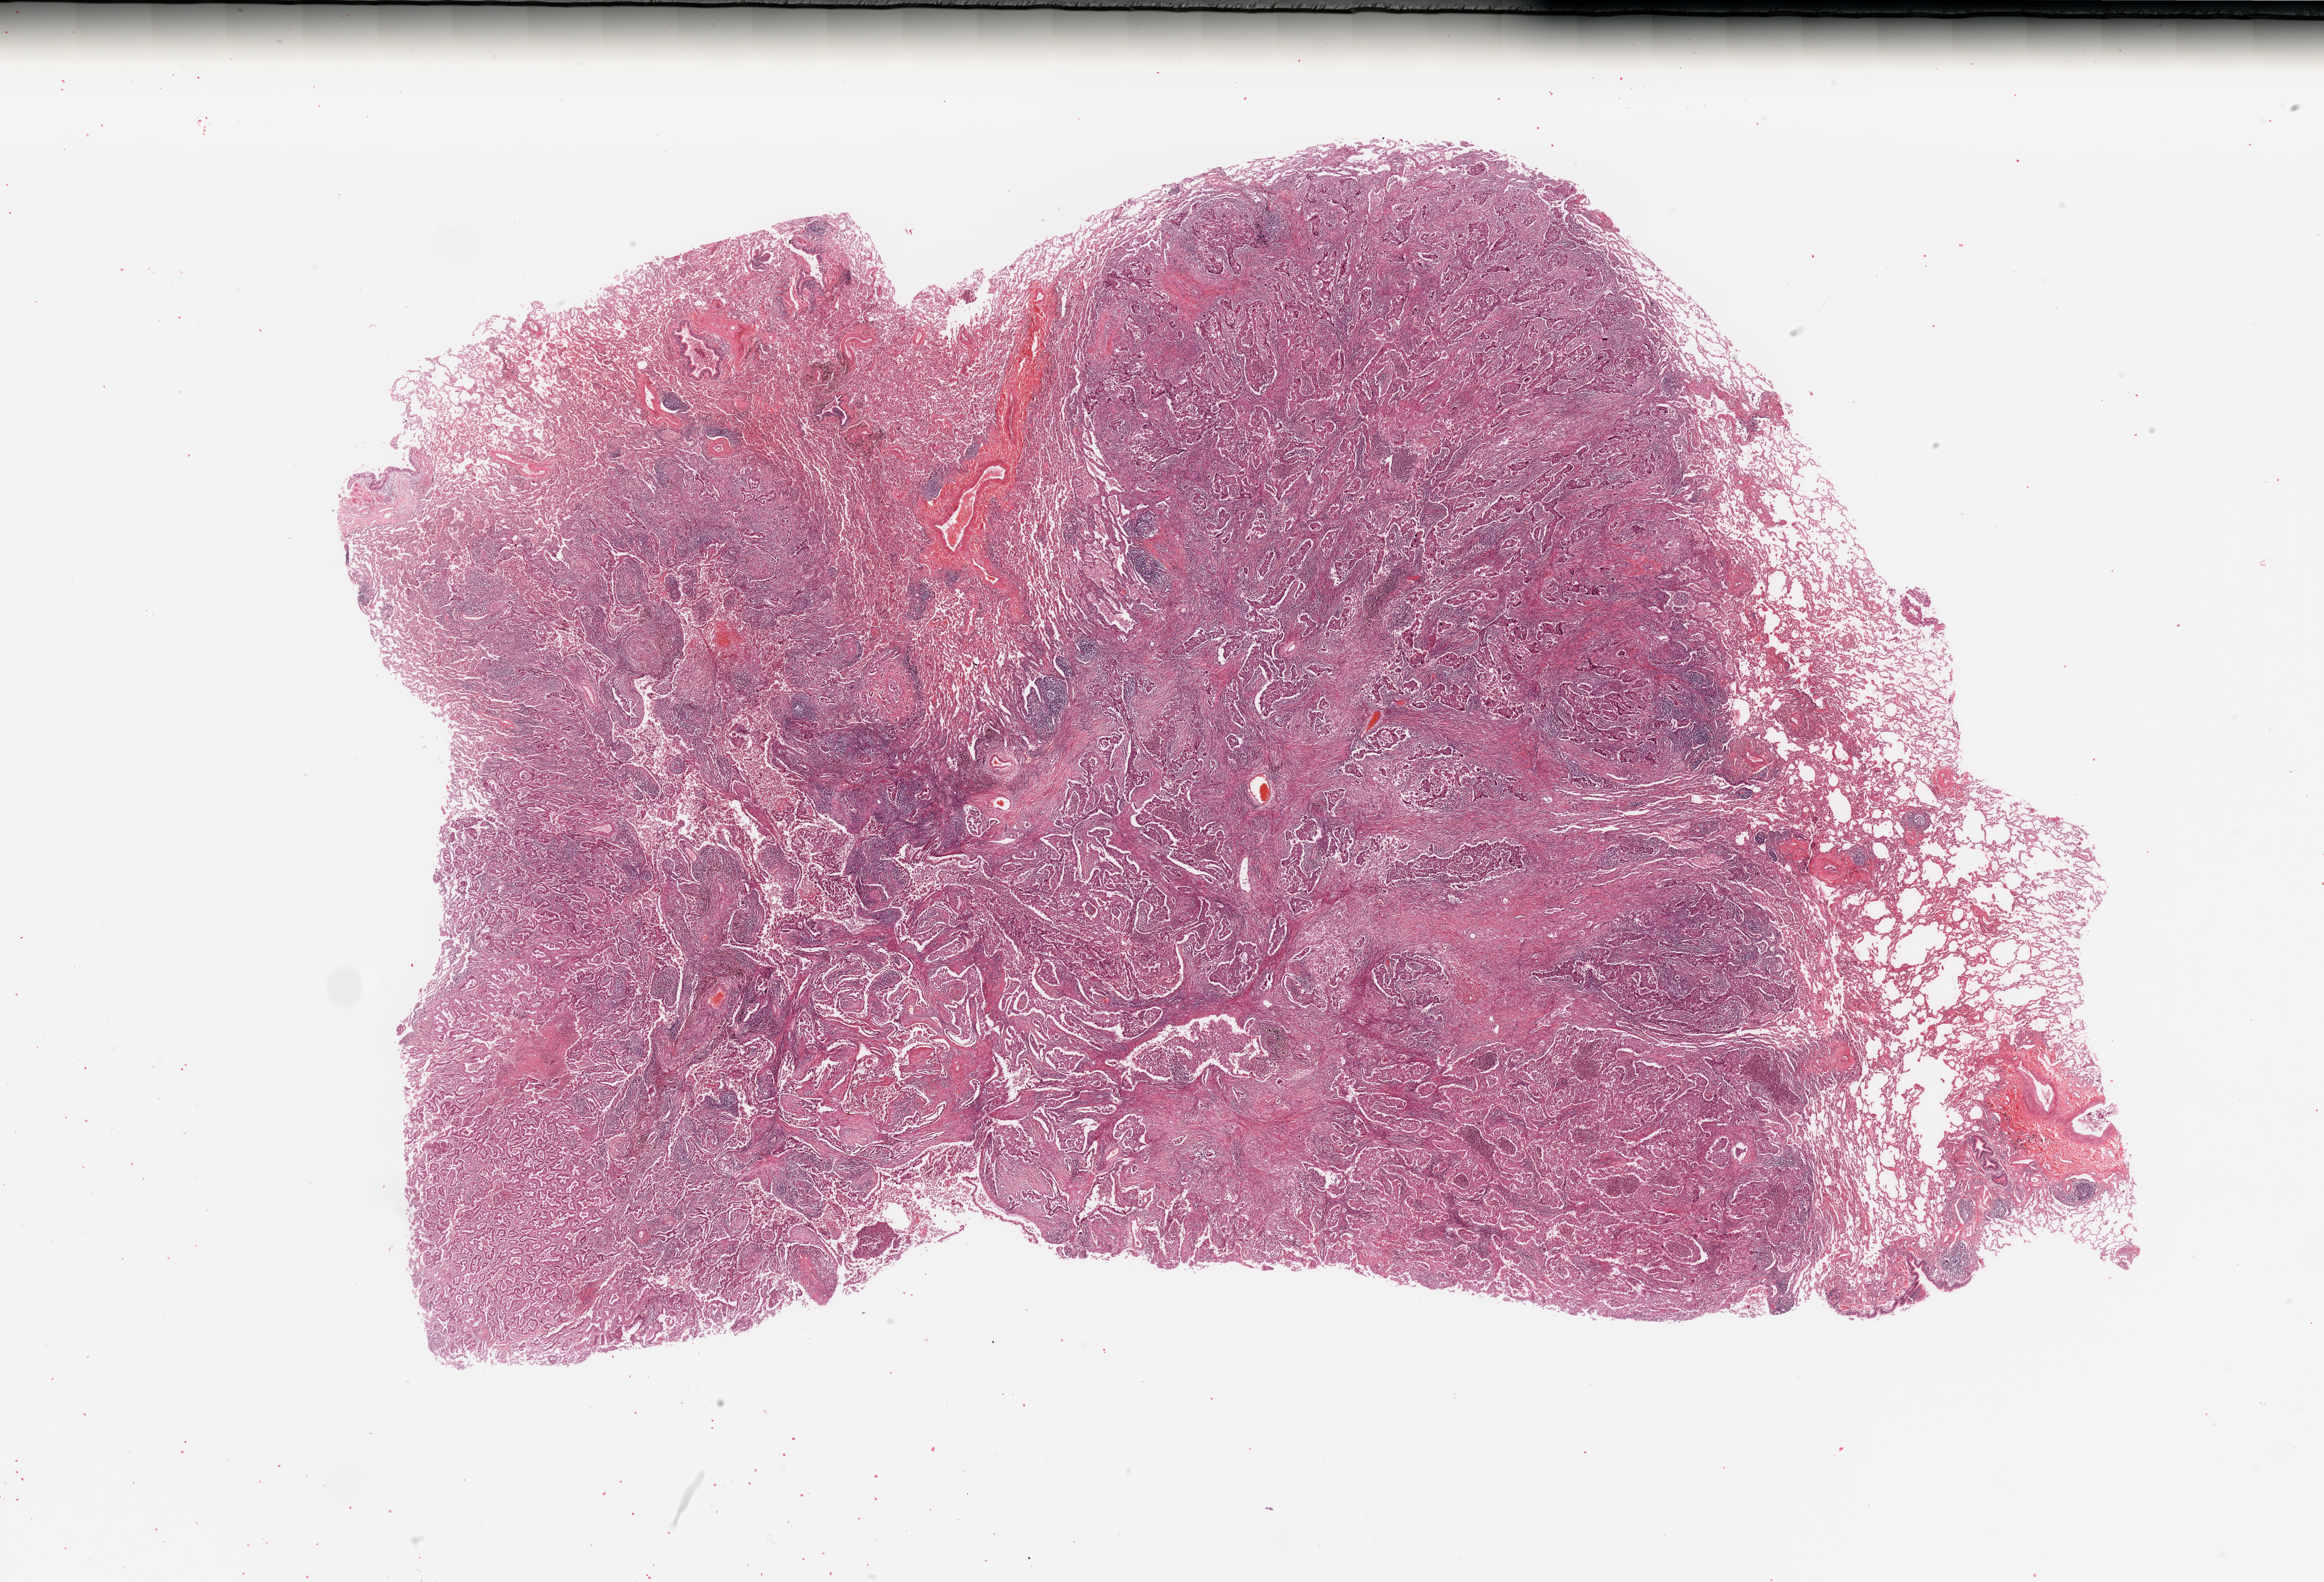
Whole-slide histology image, H&E-stained — shown as a low-resolution overview of the whole scanned area (about 30.5 x 20.8 mm, acquisition: 20x scan), tumour tissue sample, lung. Patient: female, age 61 years. Histologic grade: G3 (poorly differentiated).
AJCC pathologic stage: IIIA. Diagnosis: Adenocarcinoma, NOS.